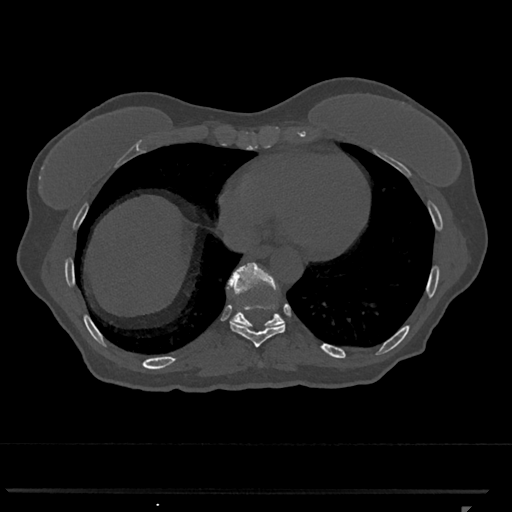
CT including the spine, one axial slice. Slice 604 of 793 in the series (ordered by position). Reconstruction kernel Br40s/3. Bone window (W 1800 / L 400 HU). 0.5 mm slice thickness. 512 × 512 image matrix, field of view 380 × 380 mm. Patient: female, 62 years. From the clinical record (not read from this slice): primary cancer: renal.
Annotated regions visible in this slice (semi-automatically segmented with operator editing):
- T10 vertebra: box from (x=227, y=263) to (x=285, y=327) px
- T9 vertebra: (x=230, y=303)–(x=286, y=347)